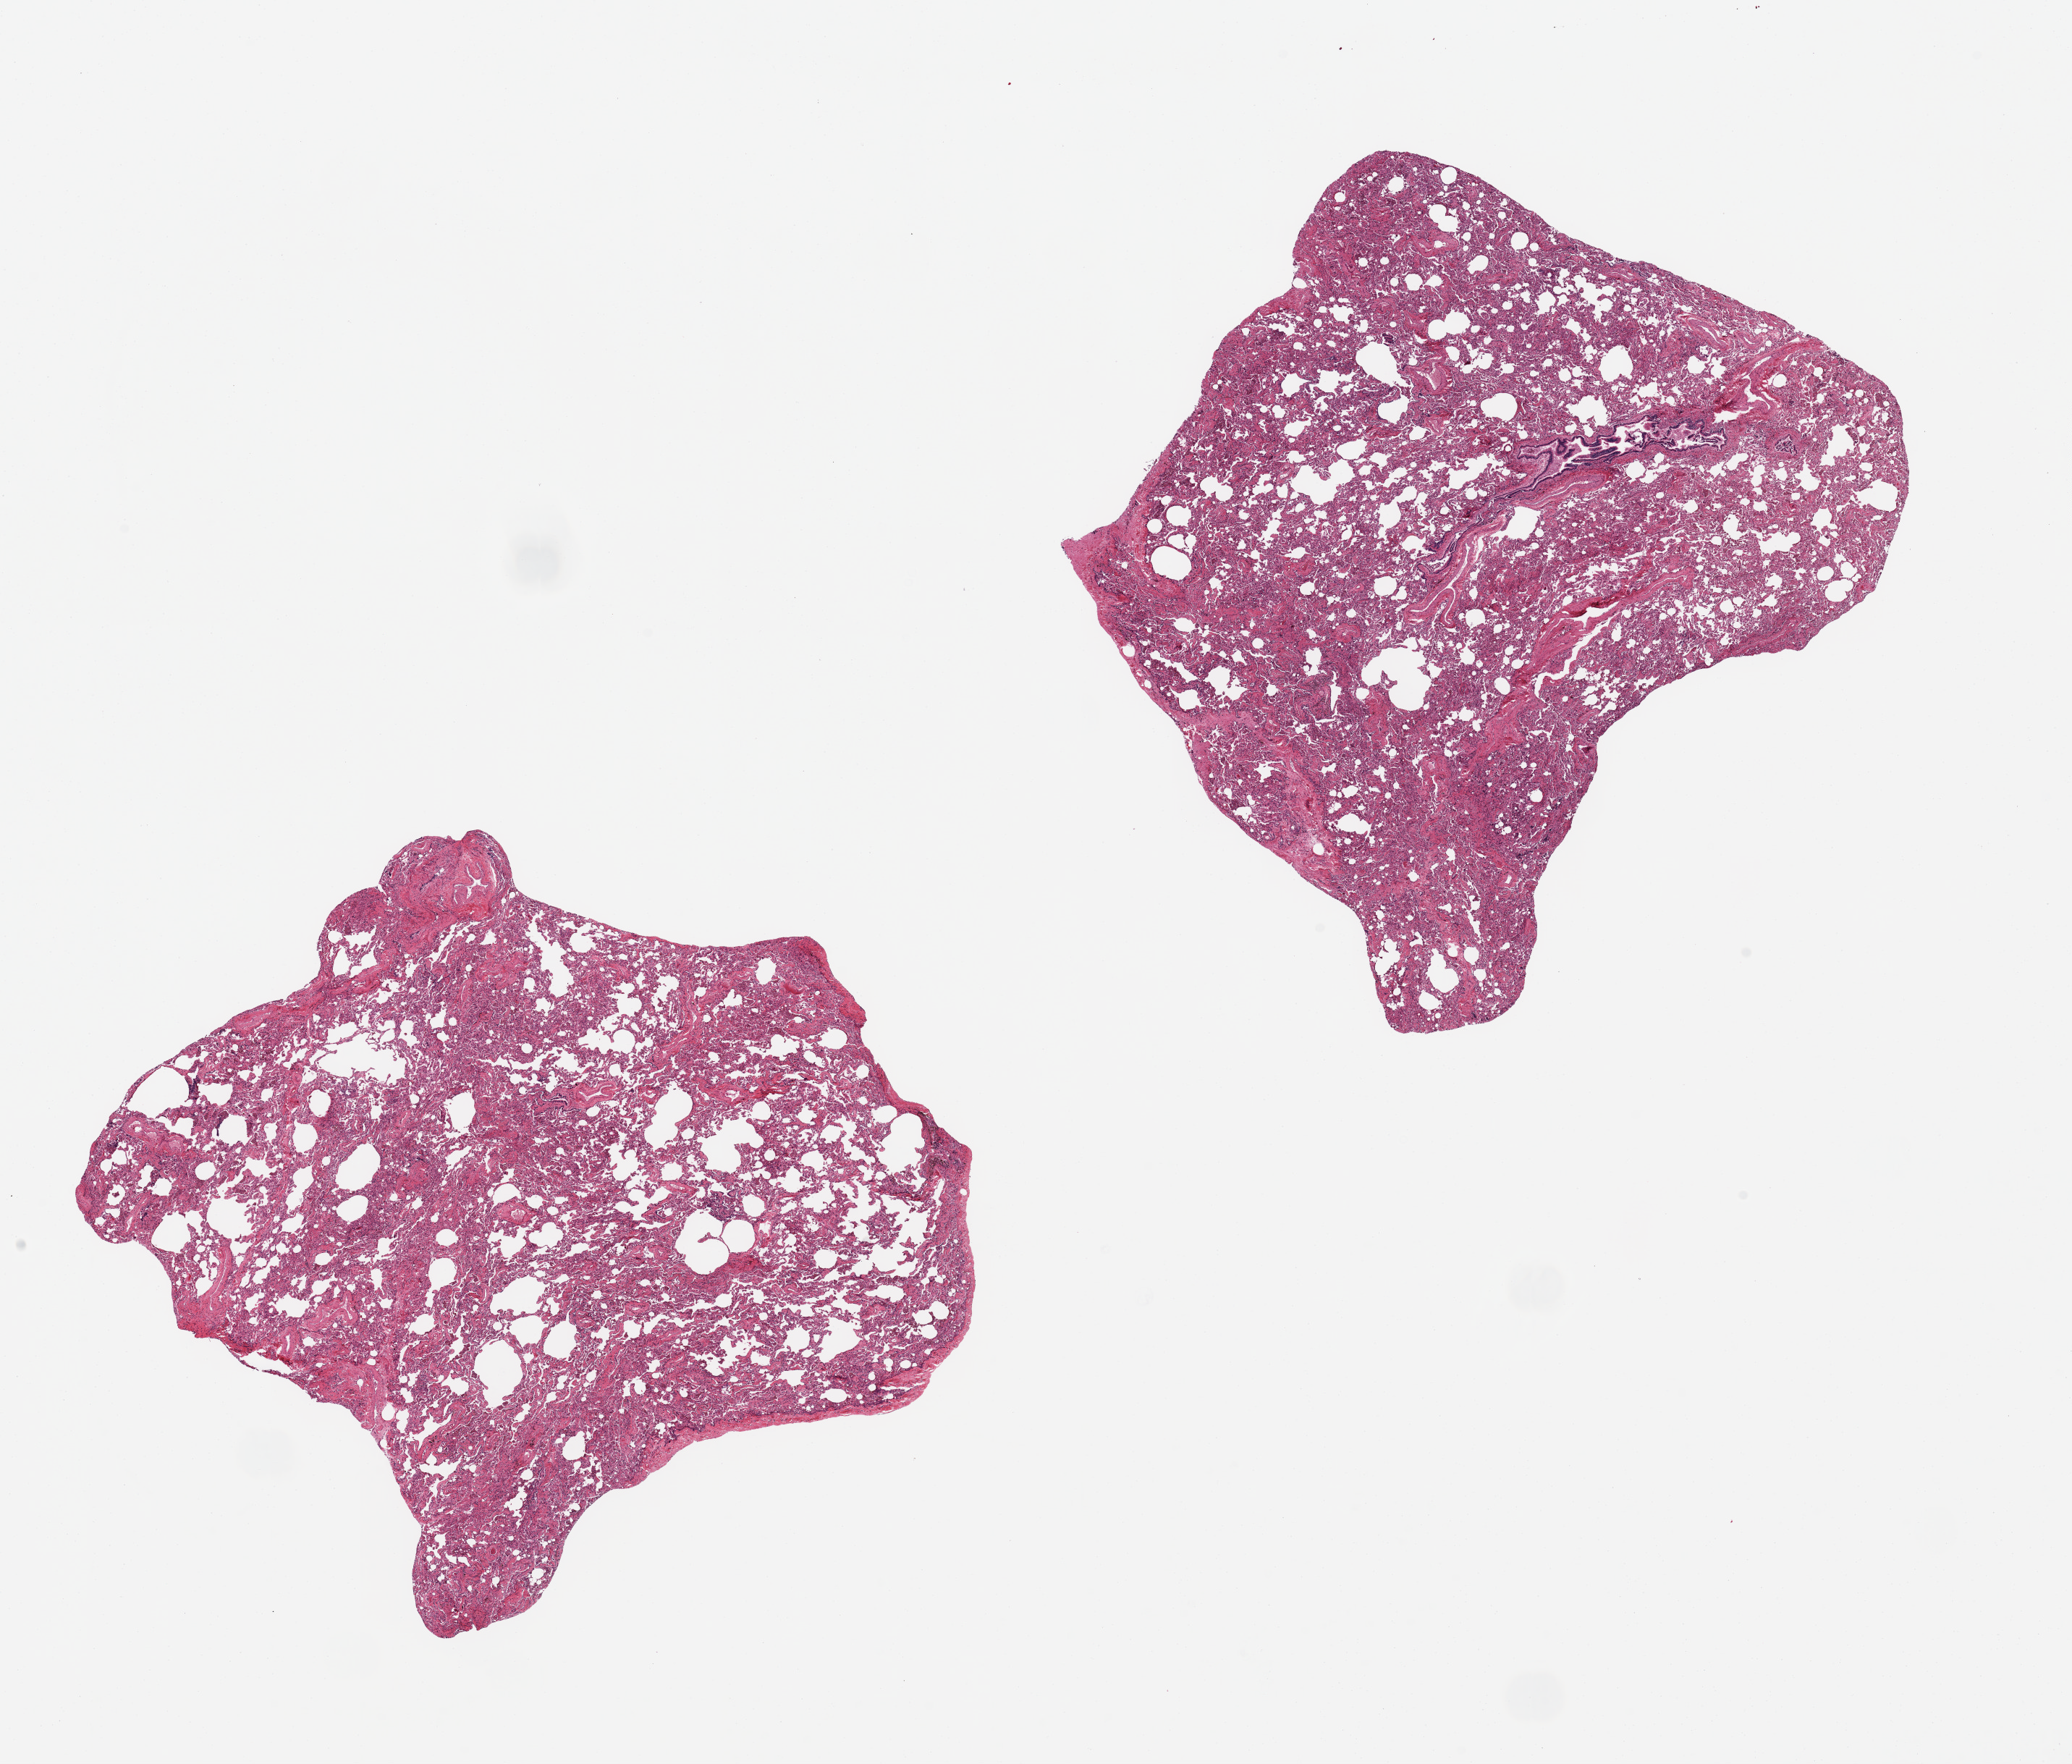
Digitized H&E-stained section — shown as a low-resolution overview of the whole scanned area (about 22.6 x 19.3 mm, acquisition: 20x scan), PAXgene-fixed paraffin-embedded (PFPE) section, sampled site (target tissue): lung, donor tissue sample. Donor: female.
• pathologist's review note for this sample: 2 ~8 mm pieces. Emphysema, fibrosis